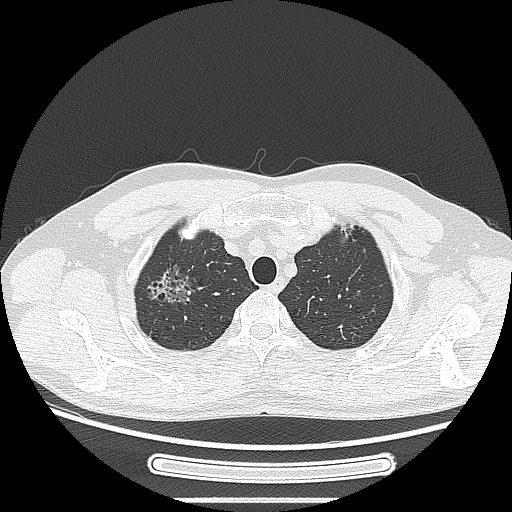
Chest CT, one axial slice; 120 kVp; lung window (W 1500 / L -600 HU); 512 × 512 image matrix, field of view 382 × 382 mm. Male patient, age 53 years. From the clinical record (not read from this slice): clinical TNM (as recorded): T1c N0 M0; histopathological grade: G2.
Outlined on this slice (bounding box drawn by a radiologist):
- lung tumour (recorded histology: adenocarcinoma): bounding box (x1, y1, x2, y2) in pixels: (139, 257, 198, 314)